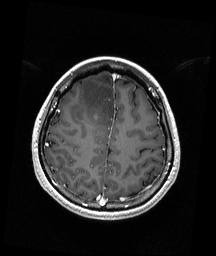
Brain MRI from a brain-tumour surgery series, one axial slice. Slice 53 of 192 in the series (ordered by position). T1-weighted post-contrast. 216 × 256 image matrix. From the clinical record (not read from this slice): histopathology: Astrocytoma; WHO grade: 4; IDH mutation: yes; tumour location: Right Frontal.
Structures marked on this image (manually delineated by an expert):
- tumour: bounding box [x1, y1, x2, y2] px = [93, 113, 98, 120]